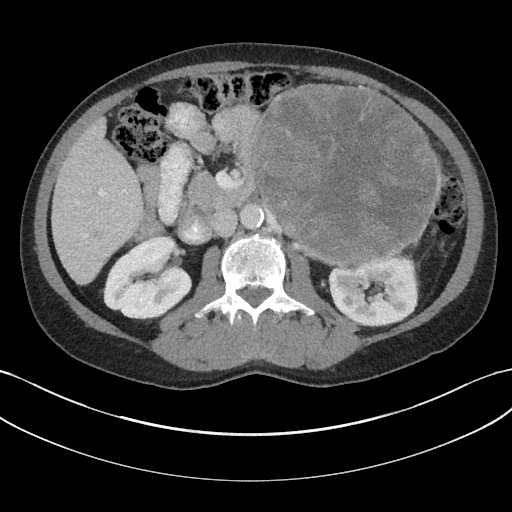
Contrast-enhanced abdominal CT, one axial slice; soft-tissue window (W 400 / L 40 HU); 3 mm slice thickness; 512 × 512 image matrix. Male patient, age 58 years. From the clinical record (not read from this slice): diagnosis: adrenocortical carcinoma; tumour side: left adrenal; tumour size at pathology: 22 cm; Ki-67 index: 26 %; stage (as recorded): 2.
Annotated regions visible in this slice (semi-automatic segmentation, software-assisted and operator-edited):
- mass: bounding box (x1, y1, x2, y2) in pixels: (253, 86, 439, 261)